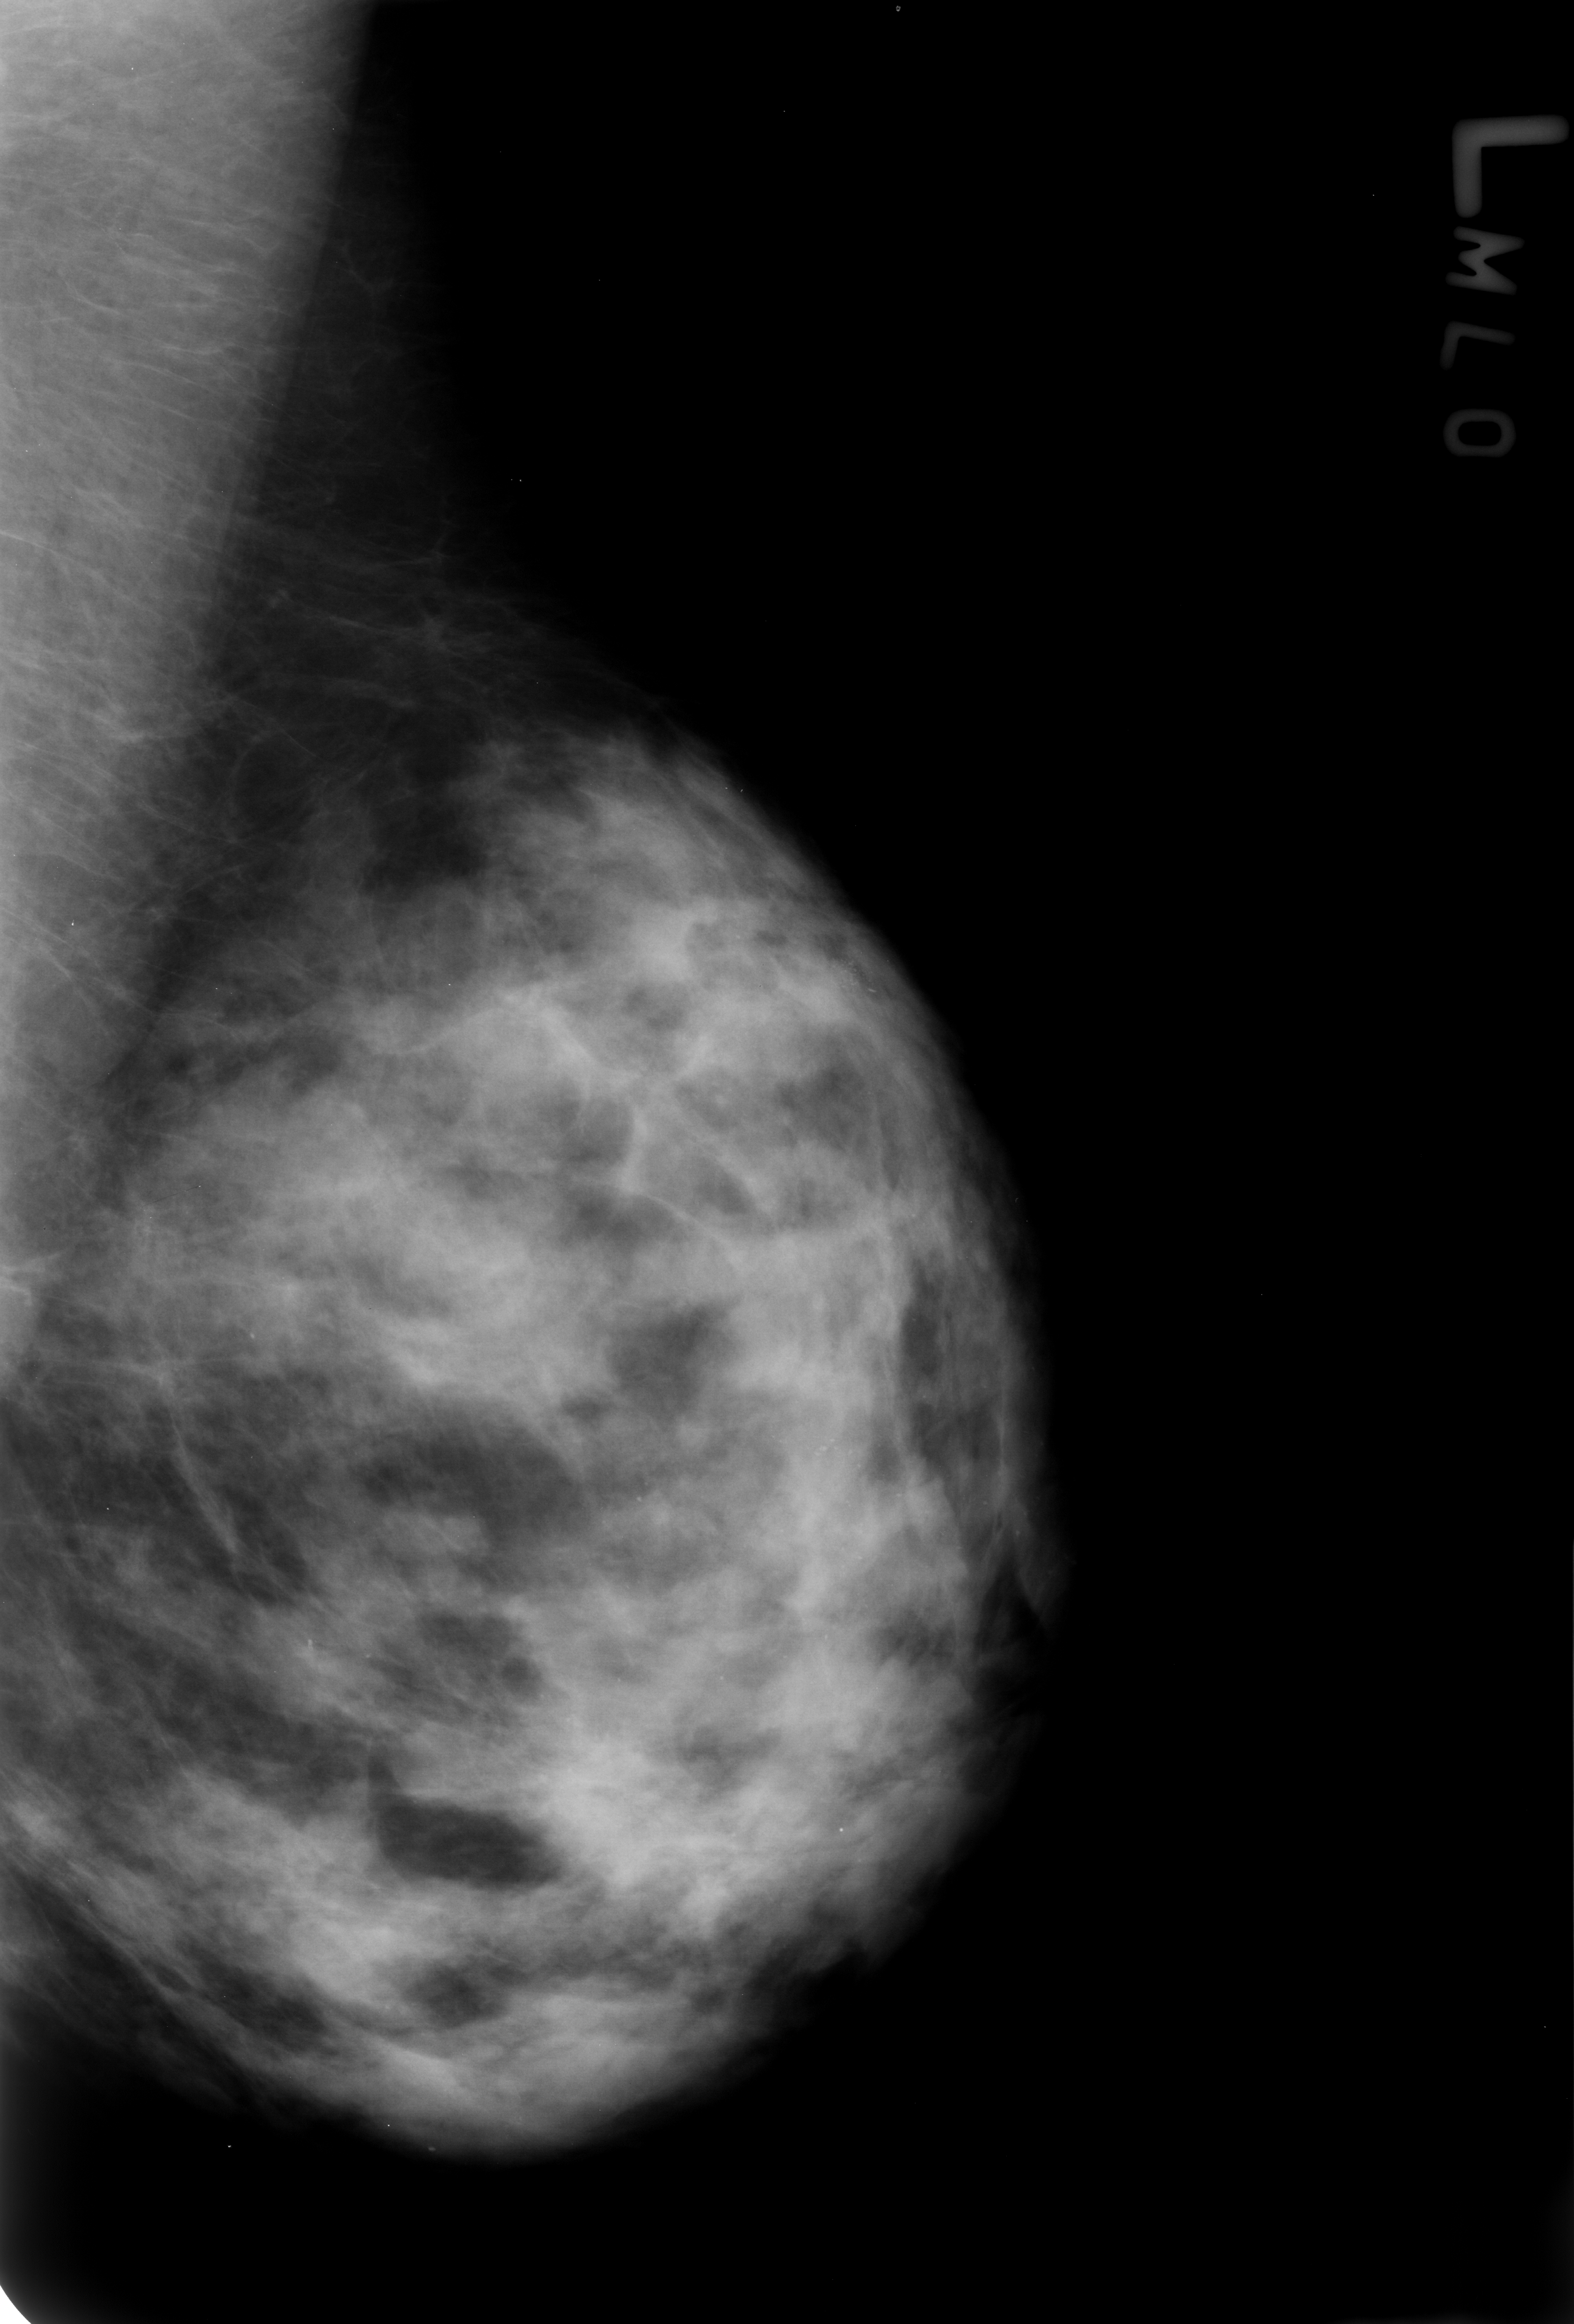
Mammogram (digitized film); left breast; MLO view; BI-RADS breast density category 3 (scale 1–4).
- Finding: calcifications, morphology pleomorphic, distribution clustered; BI-RADS assessment category 4; pathology result (as recorded, not read from the image): benign.